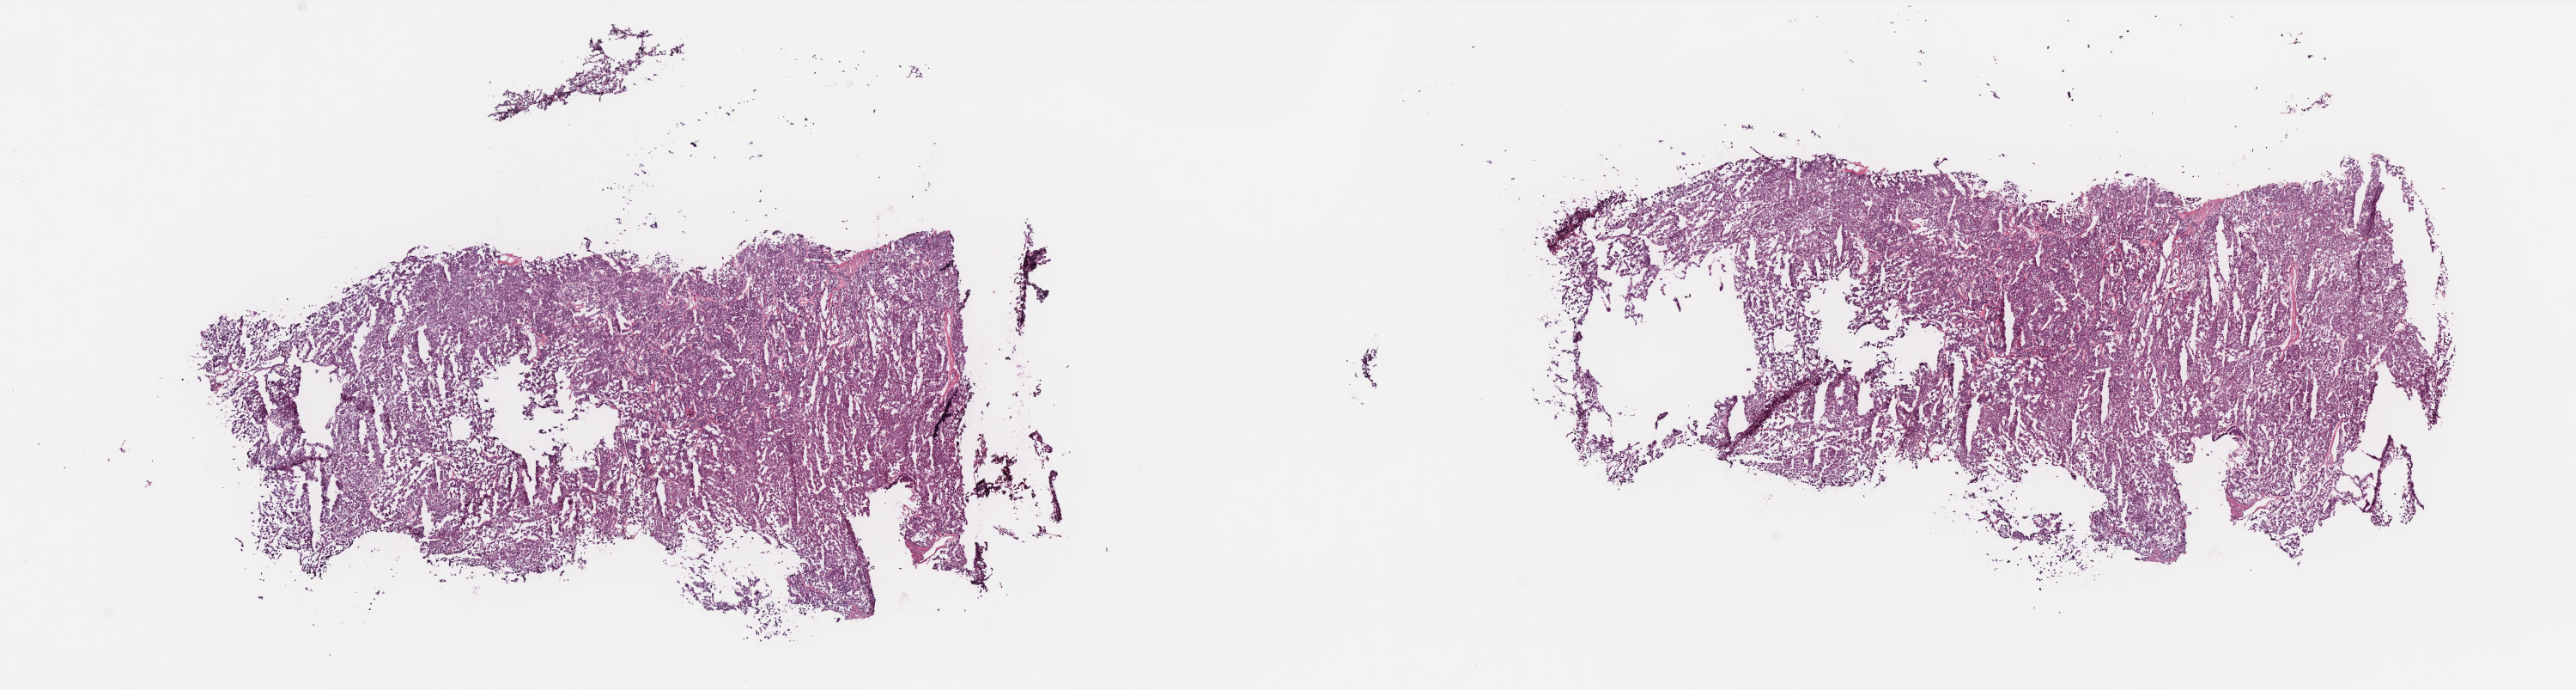
Whole-slide histology image, Hematoxylin and eosin (H&E) stained, low-resolution overview of the scanned area, about 24.1 x 6.4 mm (from a 40x scan), frozen section, kidney, primary tumour sample. Patient: male, age at initial diagnosis 44 years. Pathologist review of this section (percent, as recorded): tumour cells 80%, tumour nuclei 95%, normal cells 0%, stromal cells 0%, necrosis 20%. Infiltration values recorded for this section: lymphocyte infiltration 0%, monocyte infiltration 0%, neutrophil infiltration 0%.
TNM: T1a NX. AJCC pathologic stage: I (7th edition). Pathologic diagnosis: Renal cell carcinoma, chromophobe type.